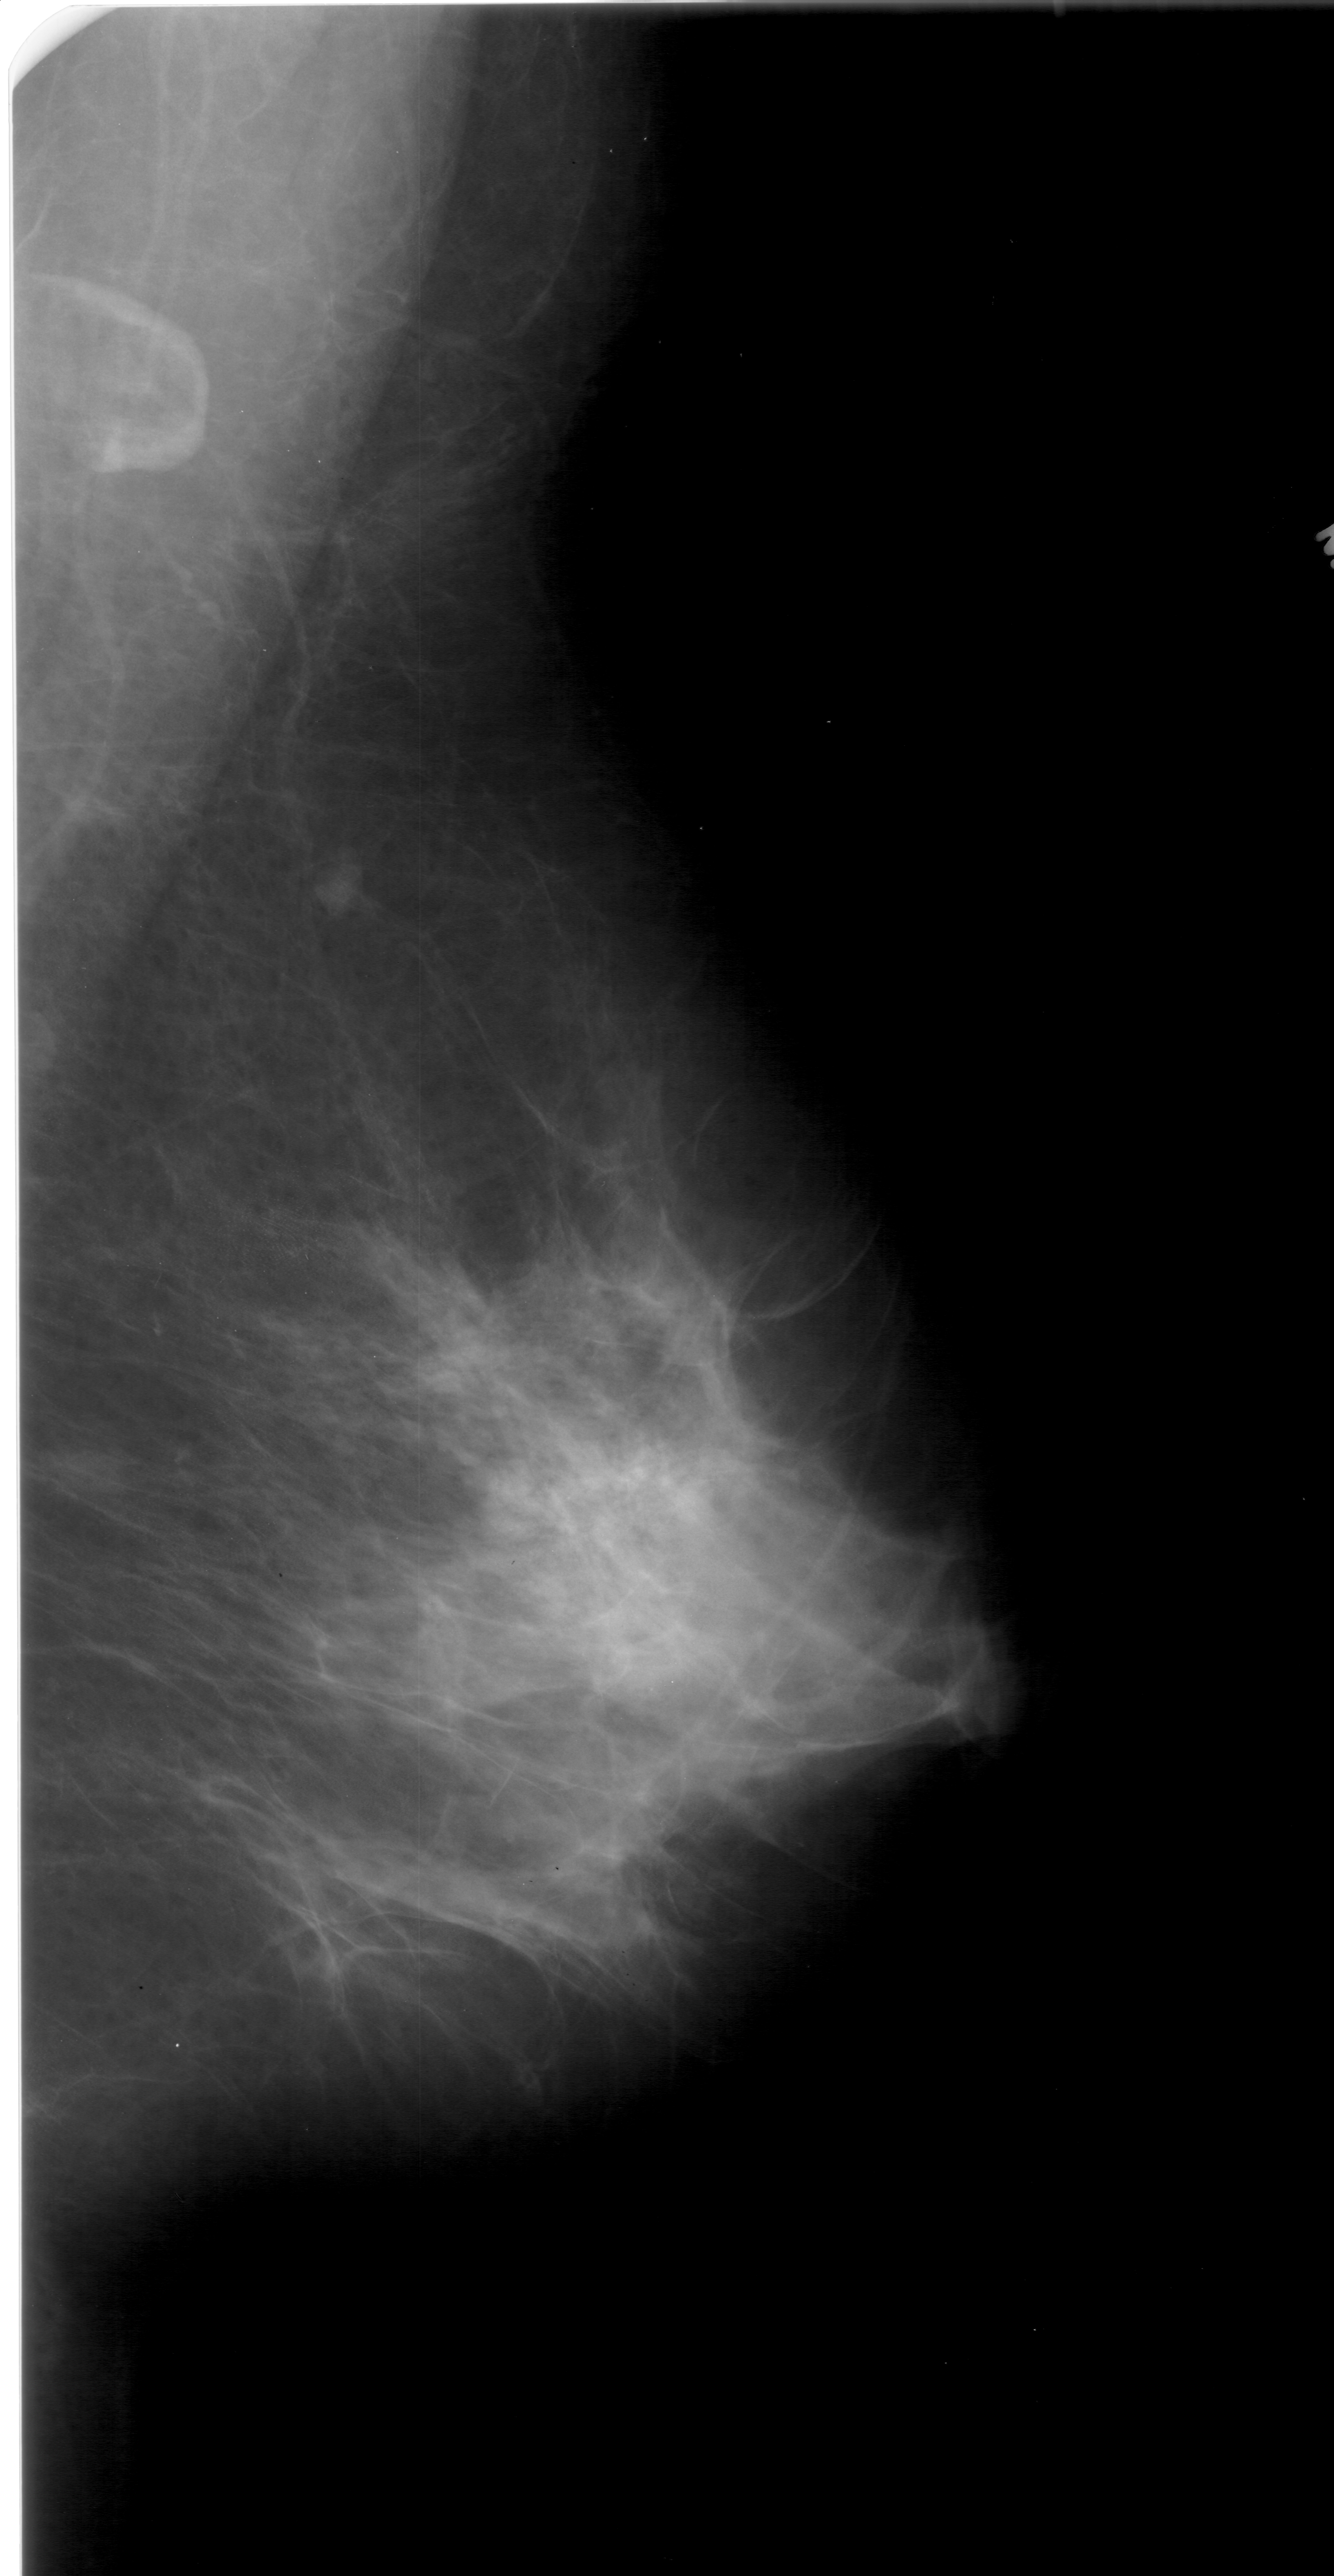
Mammogram (digitized film); right breast; mediolateral oblique (MLO) view; breast composition: extremely dense (BI-RADS density category 4 of 4); 1334 × 2576 image matrix.
Expert-marked regions of interest on this image (one box per marked abnormality):
- mass, shape architectural distortion, margins spiculated; BI-RADS assessment category 4; subtlety rating 4 on a 1 (subtle) to 5 (obvious) scale; pathology (as recorded): benign: bounding box (x1, y1, x2, y2) in pixels: (479, 1401, 719, 1633)